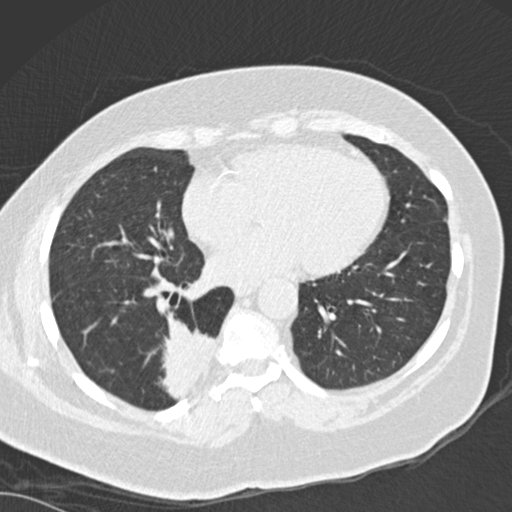
Chest CT (low-dose screening protocol), one axial image, baseline screening round, lung window (W 1500 / L -600 HU), slice 99 of 162 in the series. Female participant, aged 66 years at enrolment.
Lesion marked by an expert reader, box from (x=148, y=319) to (x=229, y=402) px. The screening reader recorded 3 non-calcified nodules or masses ≥4 mm on this exam (left lower lobe, left lower lobe, right lower lobe); which of them this box marks is not recorded. Official screen result: positive, change unspecified: nodule(s) >= 4 mm or enlarging nodule(s), mass(es), or other non-specific abnormalities suspicious for lung cancer. Participant outcome: lung cancer diagnosed 67 days after this screen — adenocarcinoma, NOS, right lower lobe, well differentiated (G1), stage IB (AJCC 6th edition), 55 mm at pathology.